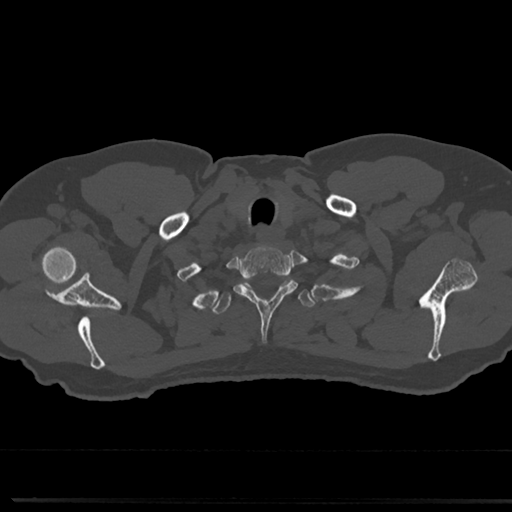
CT including the spine, one axial slice; position 663 of 817 along the scan axis; reconstruction kernel Br40s/3; bone window (W 1800 / L 400 HU); 0.5 mm slice thickness; 512 × 512 image matrix, field of view 355 × 355 mm. Patient: male, 61 years. Case-level facts recorded for this patient, not image findings: primary cancer: prostate.
Structures marked on this image (semi-automatically segmented with operator editing):
- T1 vertebra: bounding box (x1, y1, x2, y2) in pixels: (235, 247, 296, 309)
- T2 vertebra: (213, 278, 315, 315)